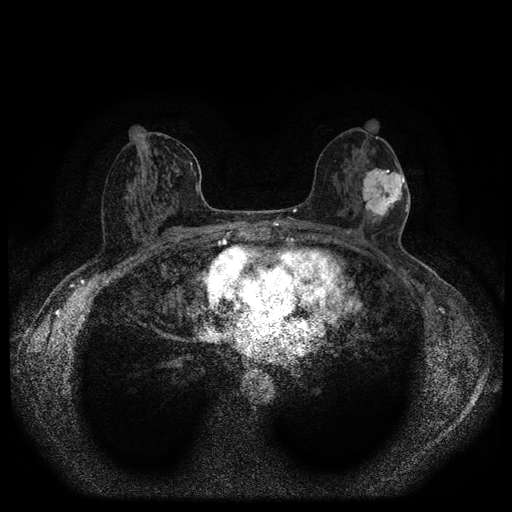
Breast MRI (dynamic contrast-enhanced, multi-phase), one axial slice; slice 54 of 116 in the series (ordered by position); dynamic contrast-enhanced series, time point 2 of 5 at this slice position (early post-contrast); 1.5 T; TE 2.7 ms, TR 5.4 ms; 2 mm slice thickness; 512 × 512 image matrix. Female patient, age 56 years.
Annotated regions visible in this slice (semi-automatic segmentation, software-assisted and operator-edited):
- breast lesion (labelled 'tumour' in the annotation; benign lesions carry a separate 'benign' label): bounding box (x1, y1, x2, y2) in pixels: (360, 164, 406, 223)